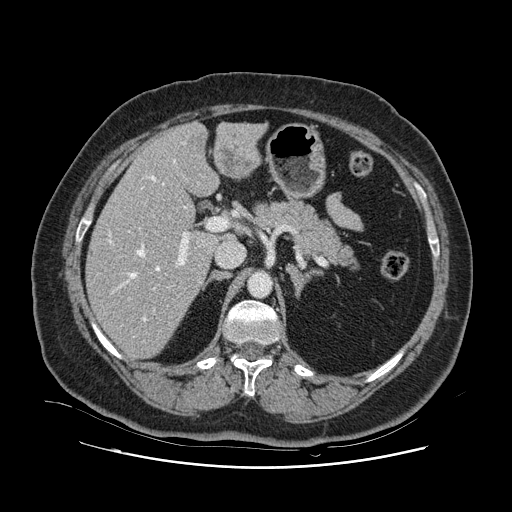
Contrast-enhanced abdominal CT, one axial slice. Position 63 of 132 along the scan axis. 120 kVp. Intravenous contrast given. Soft-tissue window (W 400 / L 40 HU). 2.5 mm slice thickness. 512 × 512 image matrix, field of view 391 × 391 mm. Female patient, age 73 years. Case-level facts recorded for this patient, not image findings: diagnosis: colorectal cancer liver metastases, imaged before liver resection; multiple liver metastases: no; largest metastasis: 7 cm; disease in both lobes: no.
Annotated regions visible in this slice (manually delineated by an expert):
- hepatic veins: box from (x=108, y=160) to (x=199, y=342) px
- liver: (x=87, y=124)–(x=261, y=358)
- planned liver remnant (the part of the liver to remain after resection): (x=87, y=150)–(x=217, y=358)
- portal vein (with intrahepatic branches): (x=128, y=218)–(x=226, y=310)
- liver metastasis: (x=219, y=148)–(x=253, y=174)